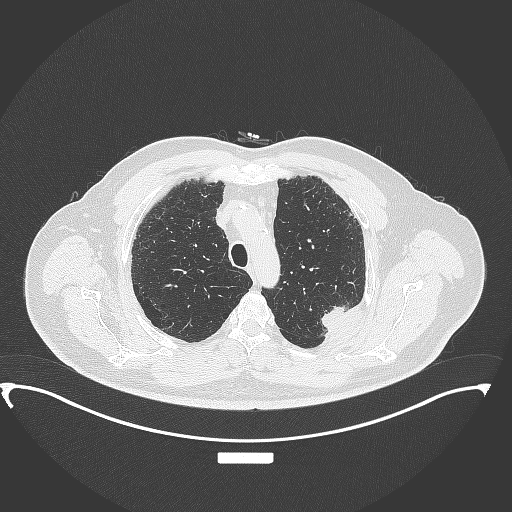
Chest CT, one axial slice. Position 283 of 350 along the scan axis. 120 kVp. Lung window (W 1500 / L -600 HU). 1 mm slice thickness. 512 × 512 image matrix. Patient: male, 64 years. From the clinical record (not read from this slice): clinical TNM (as recorded): T1c N1 M1.
Annotated regions visible in this slice (rectangle marked by the reading radiologist):
- lung tumour (recorded histology: adenocarcinoma): bounding box [x1, y1, x2, y2] px = [318, 304, 360, 340]